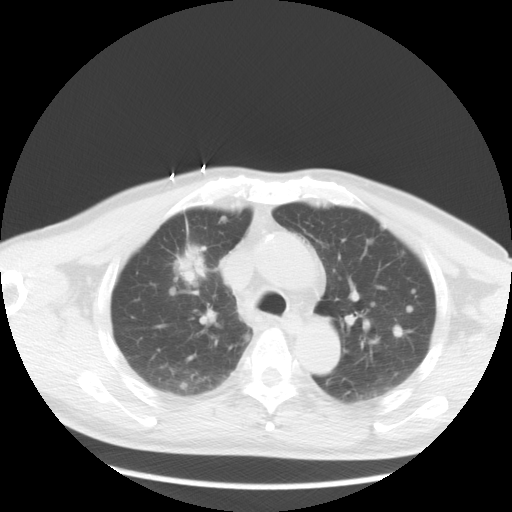
Chest CT, one axial slice; position 20 of 36 along the scan axis; reconstruction kernel STANDARD; 120 kVp; lung window (W 1500 / L -600 HU); 5 mm slice thickness; 512 × 512 image matrix, field of view 369 × 369 mm. Patient: male, 57 years. Case-level facts recorded for this patient, not image findings: clinical TNM (as recorded): T2 N3 M1a.
Annotated regions visible in this slice (rectangle marked by the reading radiologist):
- lung tumour (recorded histology: adenocarcinoma): box from (x=176, y=245) to (x=210, y=288) px